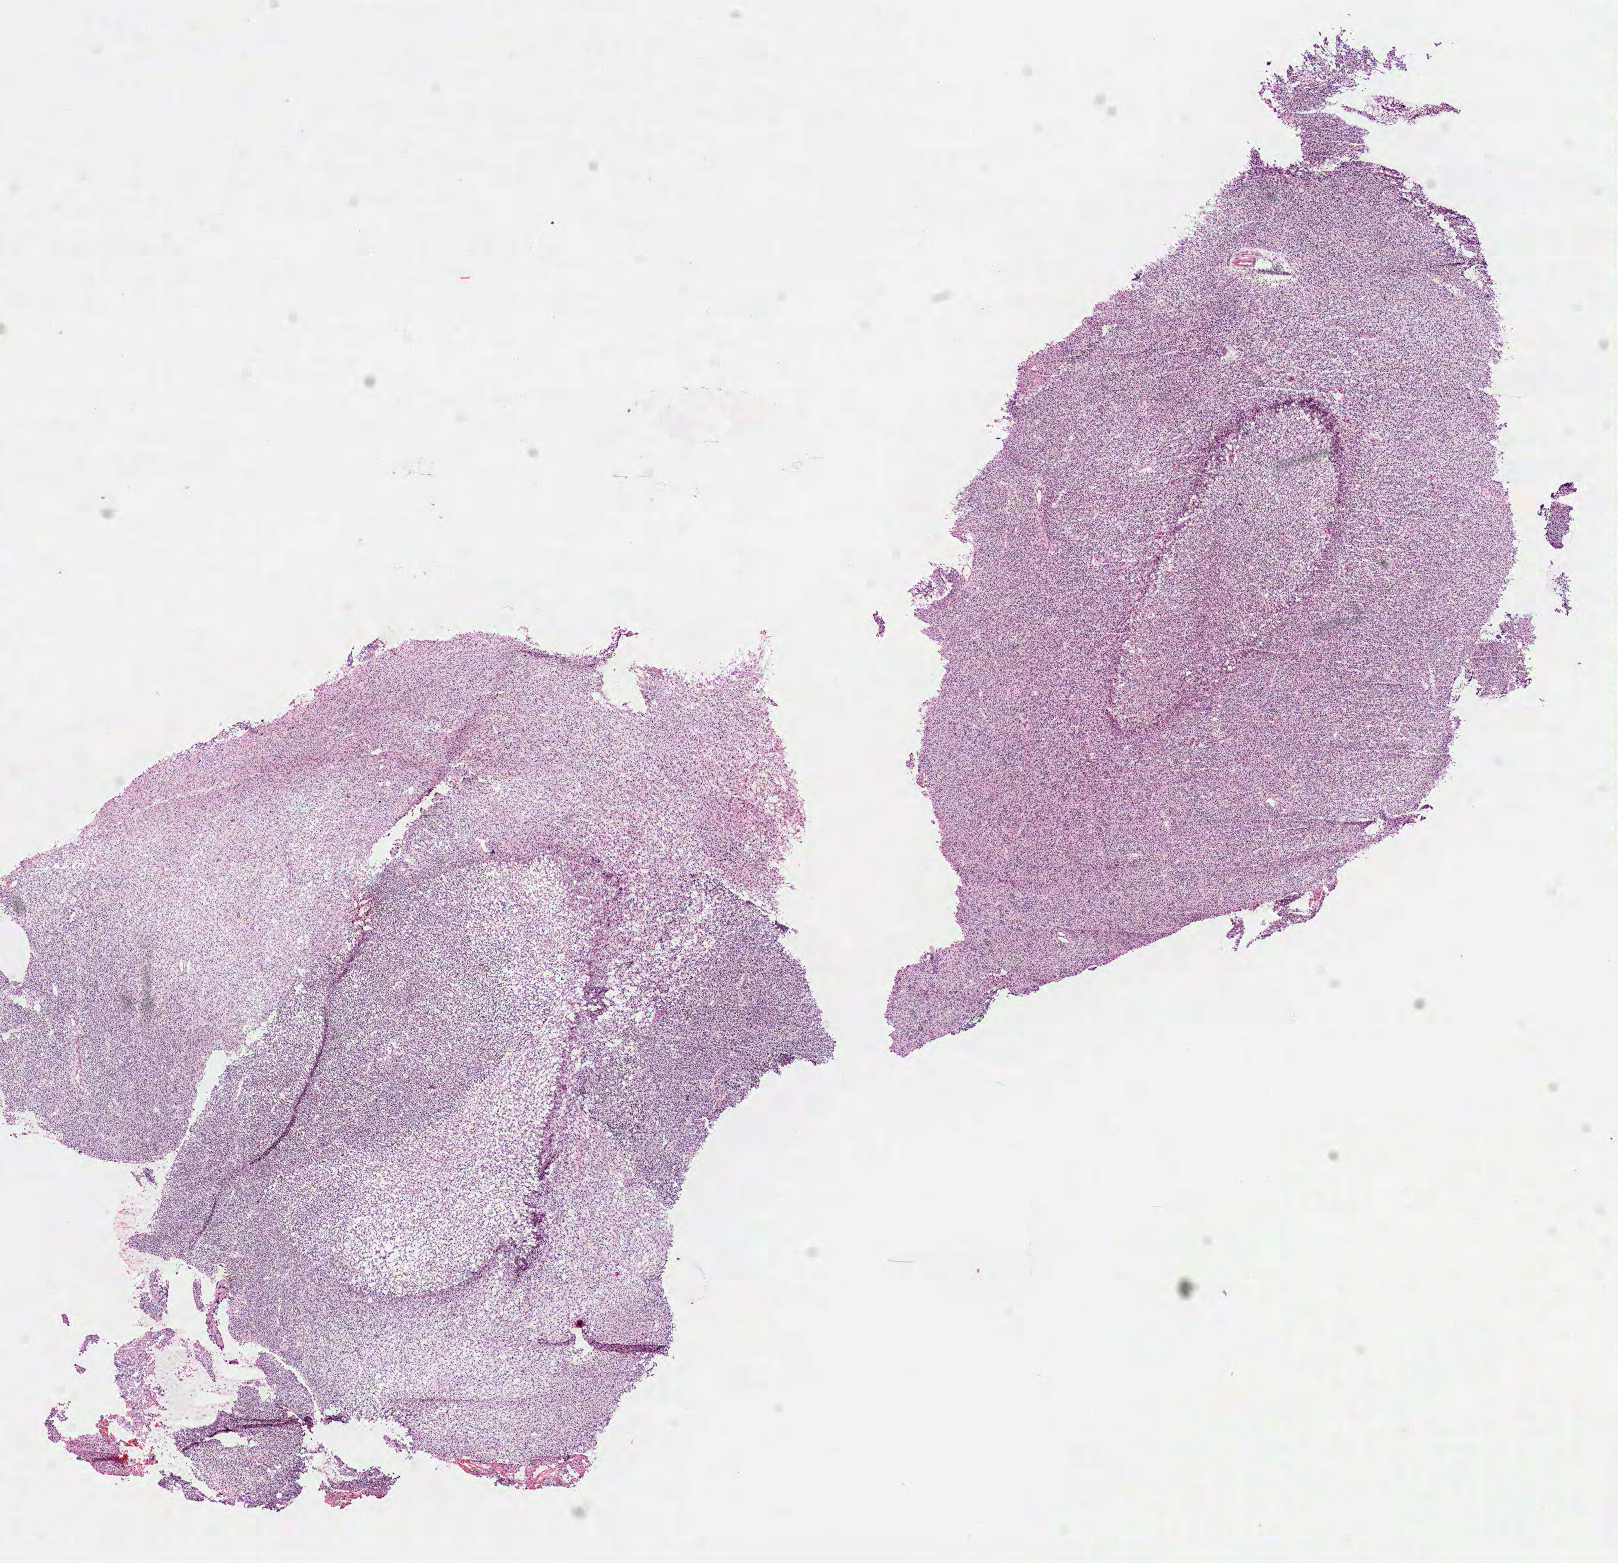
H&E-stained whole-slide image — low-resolution overview of the scanned area, about 13.1 x 12.6 mm, frozen section from the top of the tissue portion, primary tumour sample from the brain. Male patient; age at initial diagnosis 30 years. Histologic grade: G3 (poorly differentiated). Slide review estimates, as recorded: tumour cells 100%, tumour nuclei 85%, normal cells 0%, stromal cells 0%, necrosis 0%.
Diagnosis: Oligodendroglioma, anaplastic (cerebrum). Laterality: left.